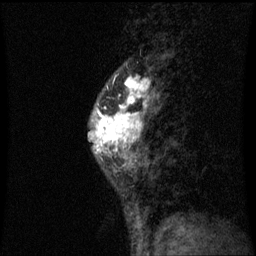
Breast MRI (dynamic contrast-enhanced), one sagittal slice. Position 24 of 60 along the scan axis. Dynamic contrast-enhanced series, image 2 of 3 at this slice position (ordered by acquisition). 1.5 T. TE 4.2 ms, TR 8.9 ms. 2 mm slice thickness. 256 × 256 image matrix. Patient: female, 50 years. Case-level facts recorded for this patient, not image findings: setting: breast cancer imaged before/during neoadjuvant chemotherapy; receptor status: triple-negative.
Outlined on this slice (semi-automatic segmentation, software-assisted and operator-edited):
- analysis volume of interest (the breast-tissue region the enhancement analysis was run in; not a lesion): bounding box (x1, y1, x2, y2) in pixels: (88, 80, 157, 171)
- tumour enhancement mask (voxels above the 70 % enhancement threshold inside the analysis volume of interest): (94, 80, 149, 153)